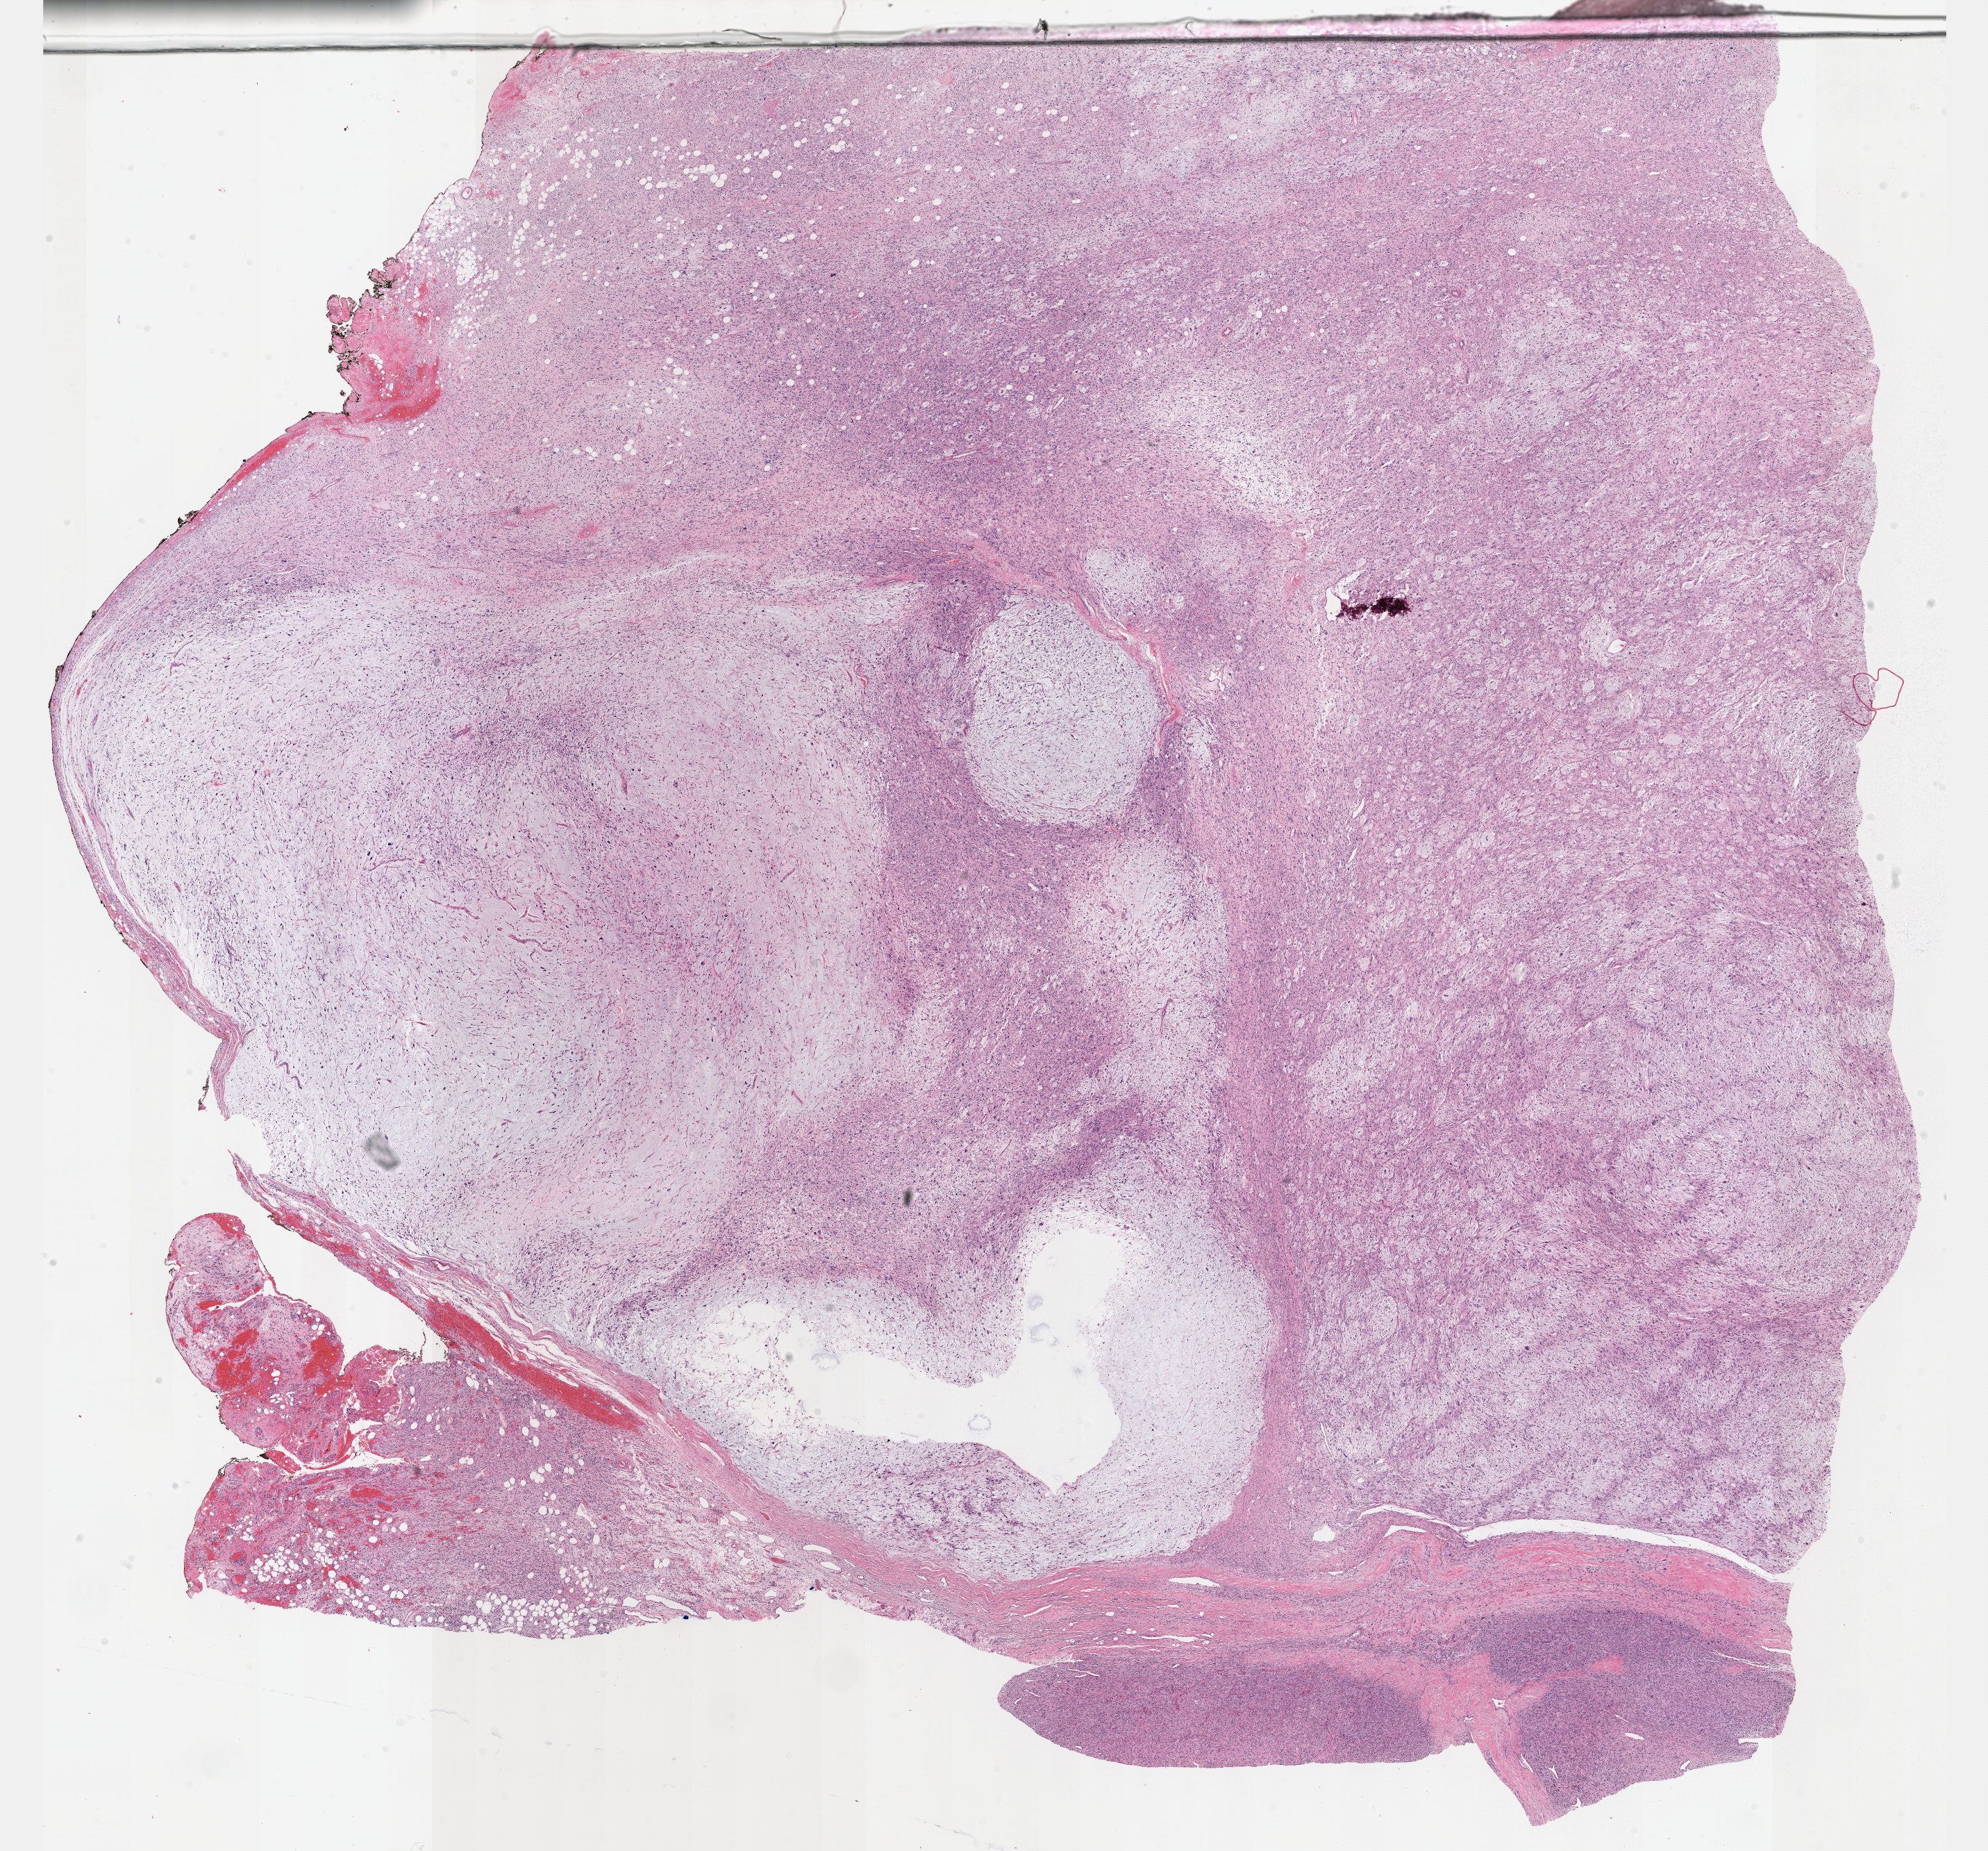
H&E-stained whole-slide image — a low-resolution overview of the entire scanned area, about 23.1 x 21.5 mm; formalin-fixed paraffin-embedded (FFPE) diagnostic section; sample: primary tumour, connective, subcutaneous and other soft tissues. Male patient; age at initial diagnosis 55 years.
- histologic diagnosis: Fibromyxosarcoma (connective, subcutaneous and other soft tissues of lower limb and hip)